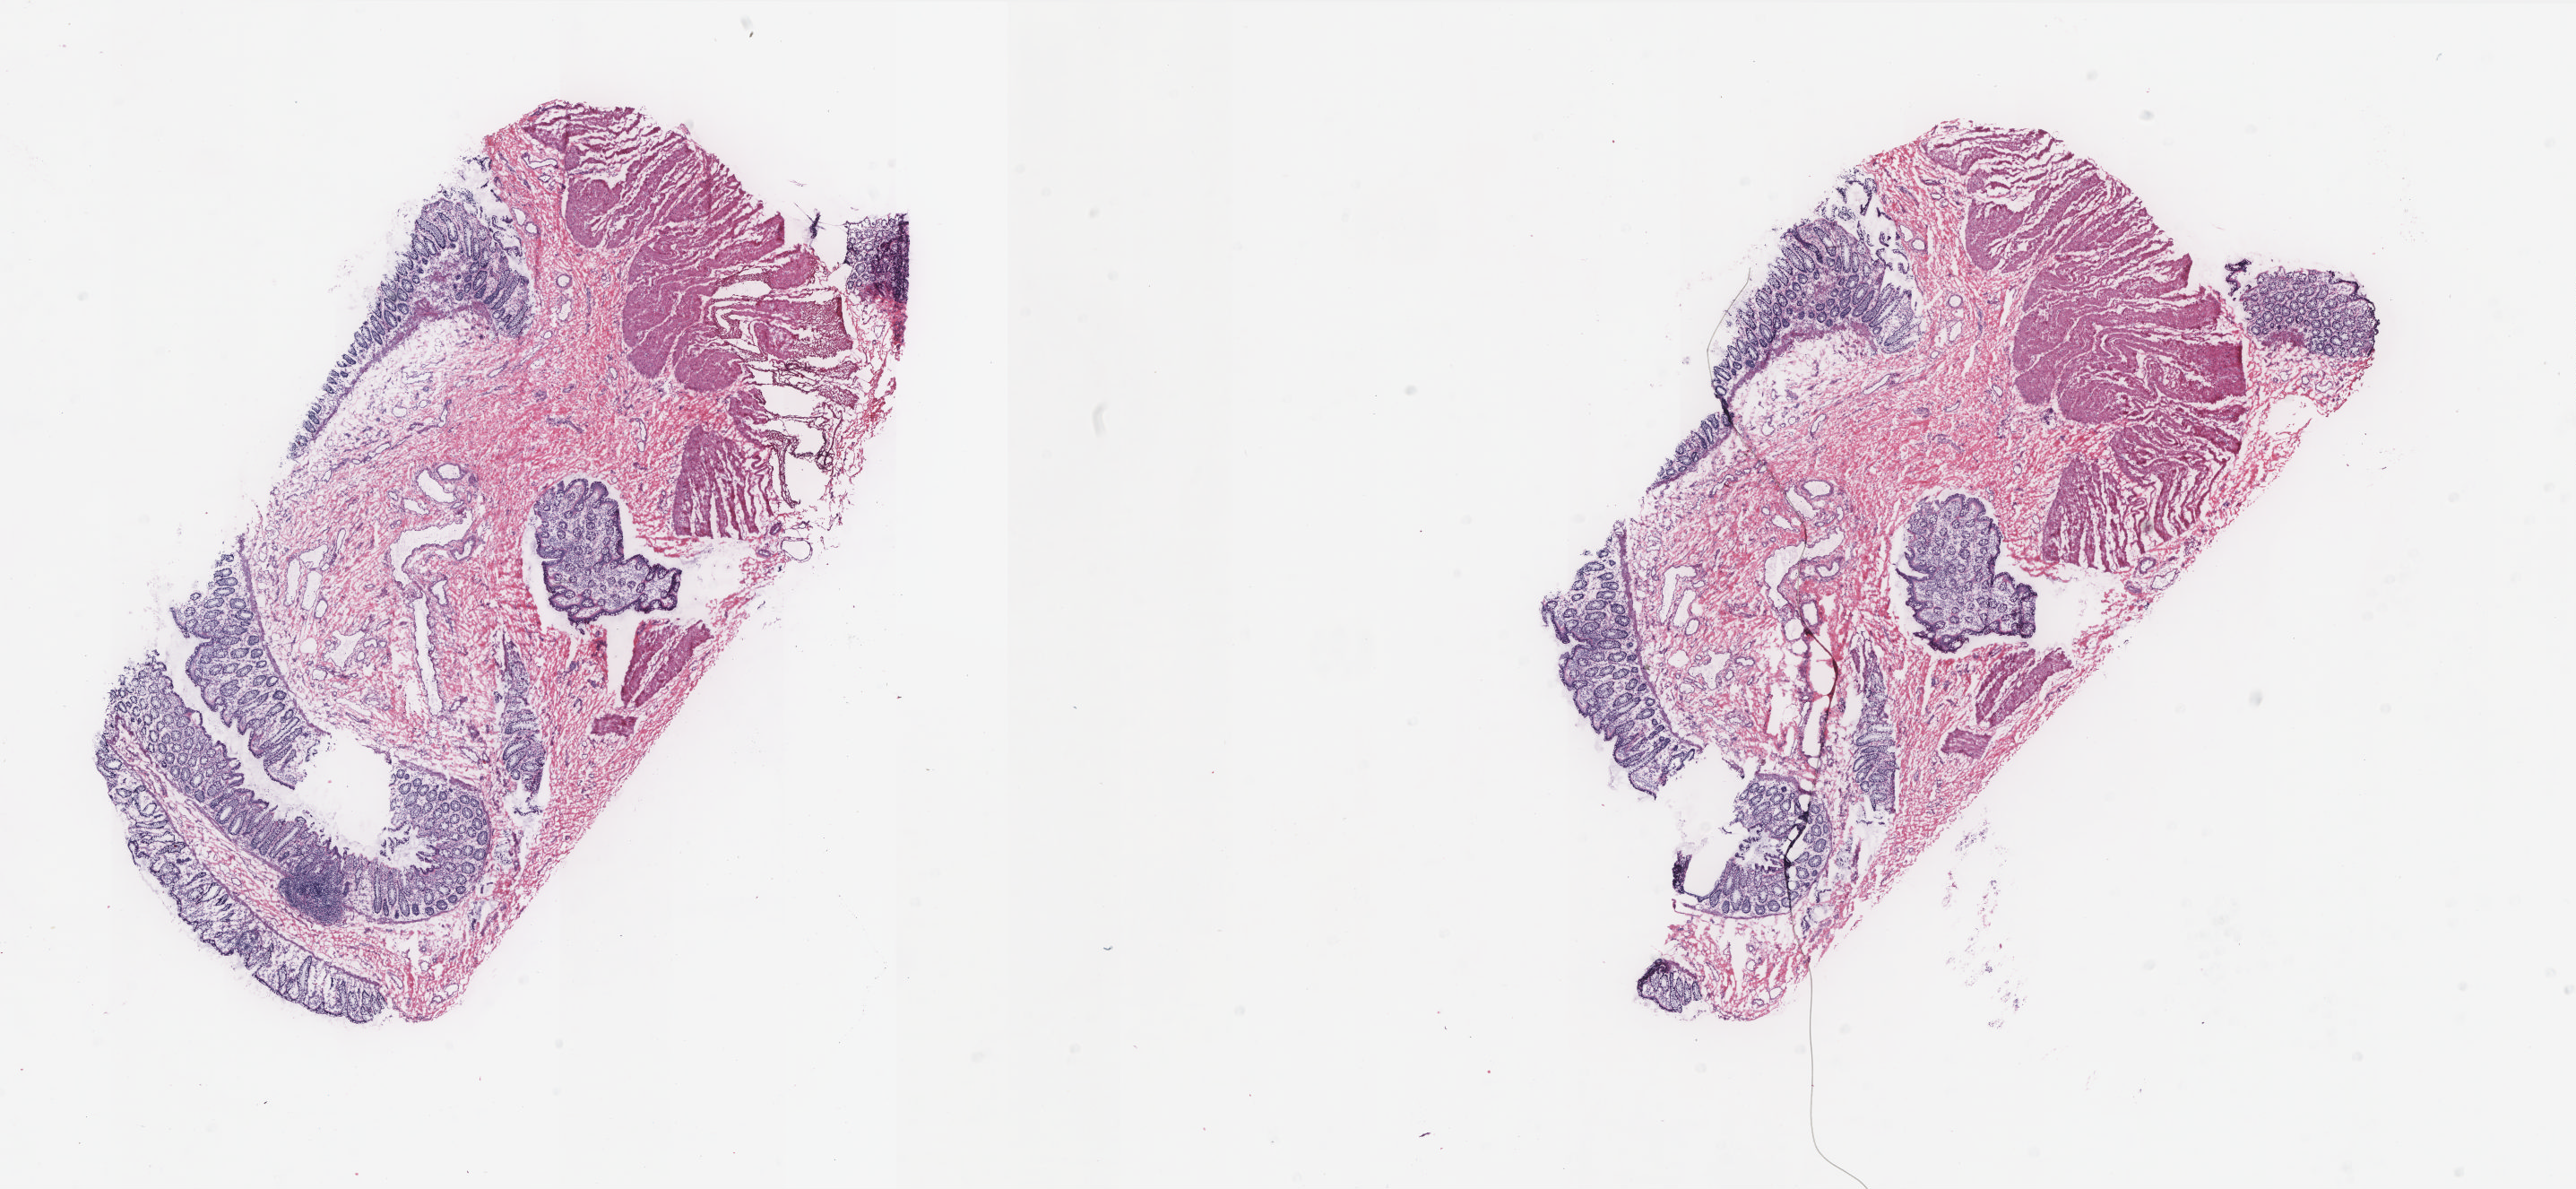
Whole-slide histology image, H&E-stained — a low-resolution overview of the entire scanned area, about 23.0 x 10.6 mm (from a 20x scan). Frozen section from the top of the tissue portion. Colon, solid tissue normal (non-tumour tissue) sample. Female patient; age at initial diagnosis 65 years. Pathologist review of this section (percent, as recorded): tumour cells 0%, normal cells 100%. Infiltration values recorded for this section: lymphocyte infiltration 30%, monocyte infiltration 6%, neutrophil infiltration 0%.
This section: solid tissue normal (non-tumour) sample from the same patient. Patient diagnosis: Adenocarcinoma, NOS (sigmoid colon).